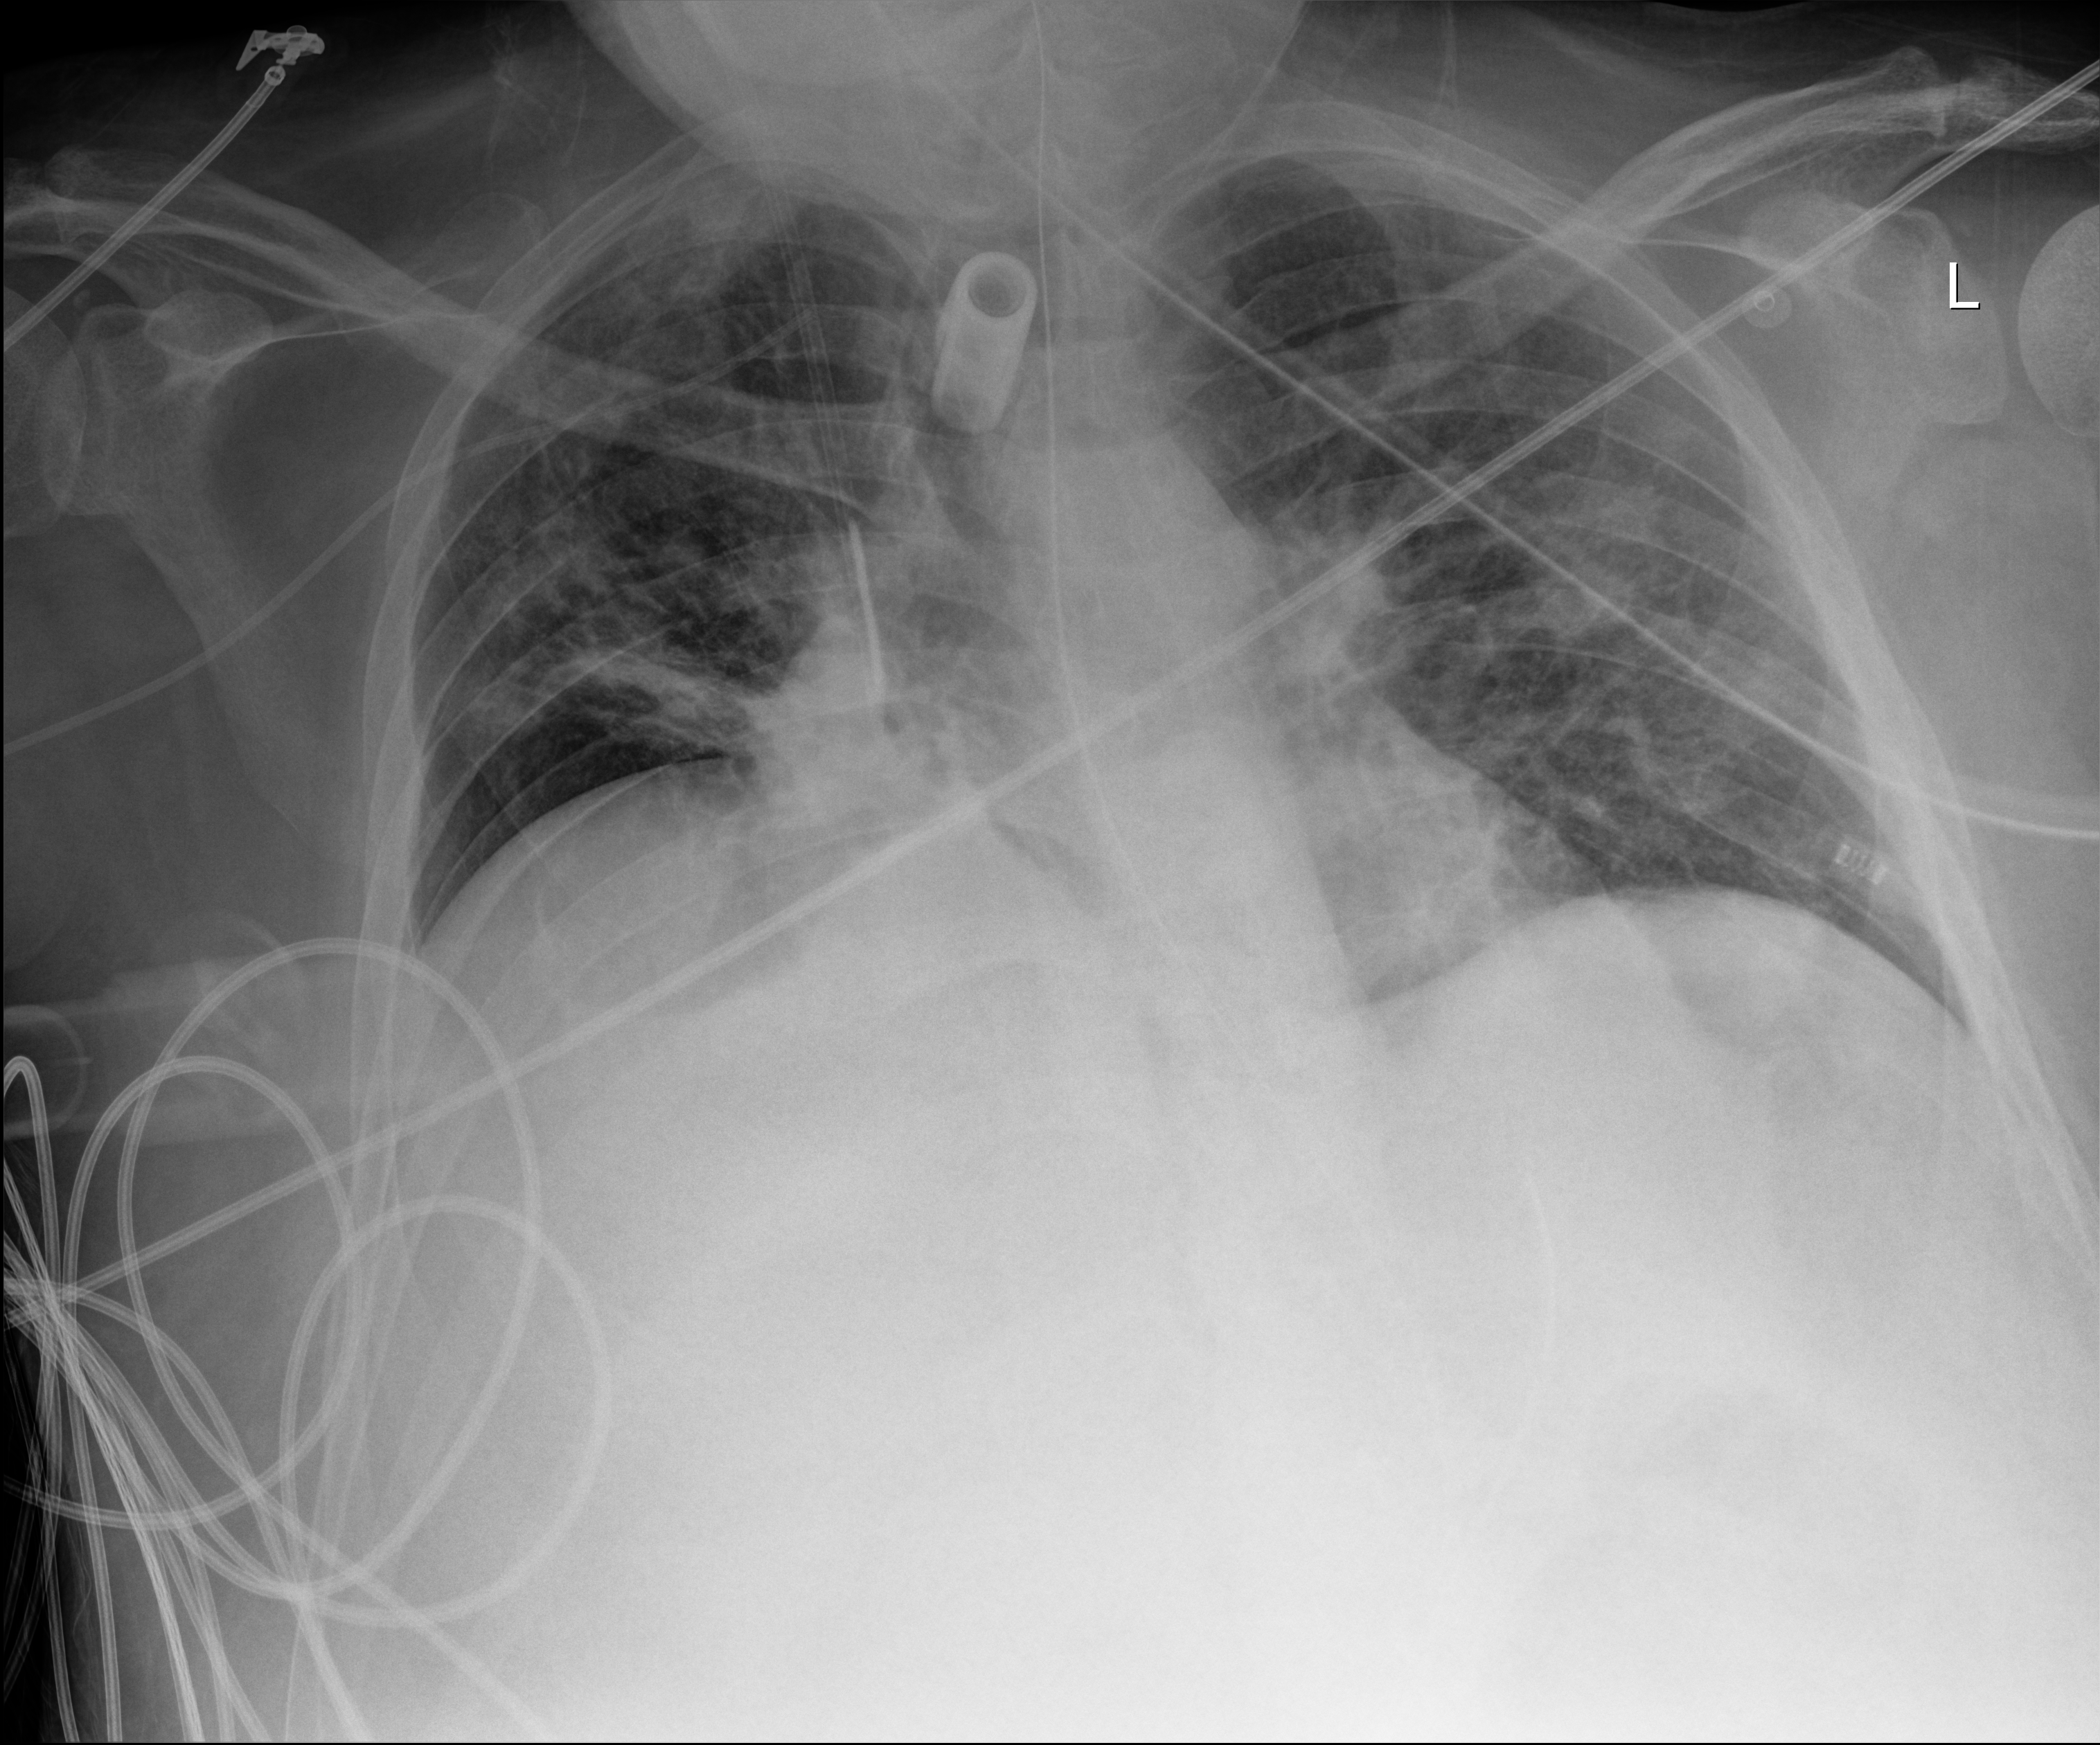
Portable chest radiograph, anteroposterior (AP) projection. Patient hospitalised with COVID-19, aged 18–59 years.
Hospital-stay facts (about this admission, not read from this image; timing relative to this image not recorded):
- mechanically ventilated during this hospital stay: yes